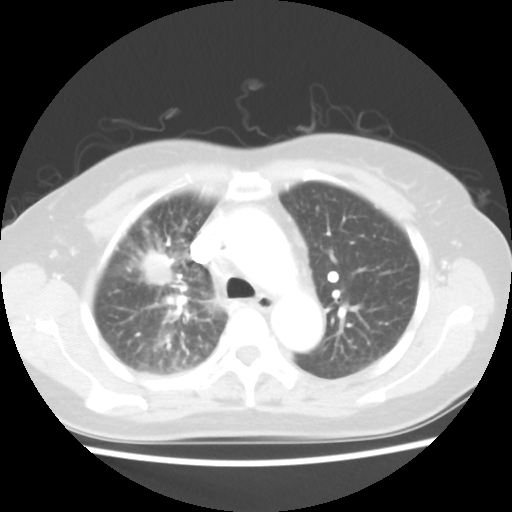
Chest CT, one axial slice. Position 32 of 48 along the scan axis. Lung window (W 1500 / L -600 HU). 5 mm slice thickness. 512 × 512 image matrix. Patient: female, 55 years. From the clinical record (not read from this slice): clinical TNM (as recorded): T1b N3 M1a.
Outlined on this slice (bounding box drawn by a radiologist):
- lung tumour (recorded histology: adenocarcinoma): box from (x=145, y=253) to (x=176, y=284) px